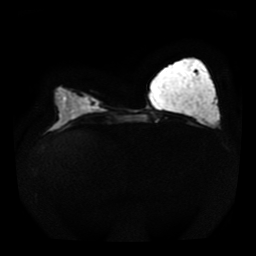
Breast MRI, one axial slice. Position 15 of 41 along the scan axis. Diffusion-weighted series; image 2 of 4 stored at this slice position (different b-values; order by instance number). 1.5 T. 5 mm slice thickness. 256 × 256 image matrix, field of view 330 × 330 mm. Female patient.
Annotated regions visible in this slice (manually delineated by an expert):
- tumour on diffusion-weighted imaging: bounding box [x1, y1, x2, y2] px = [71, 97, 93, 118]